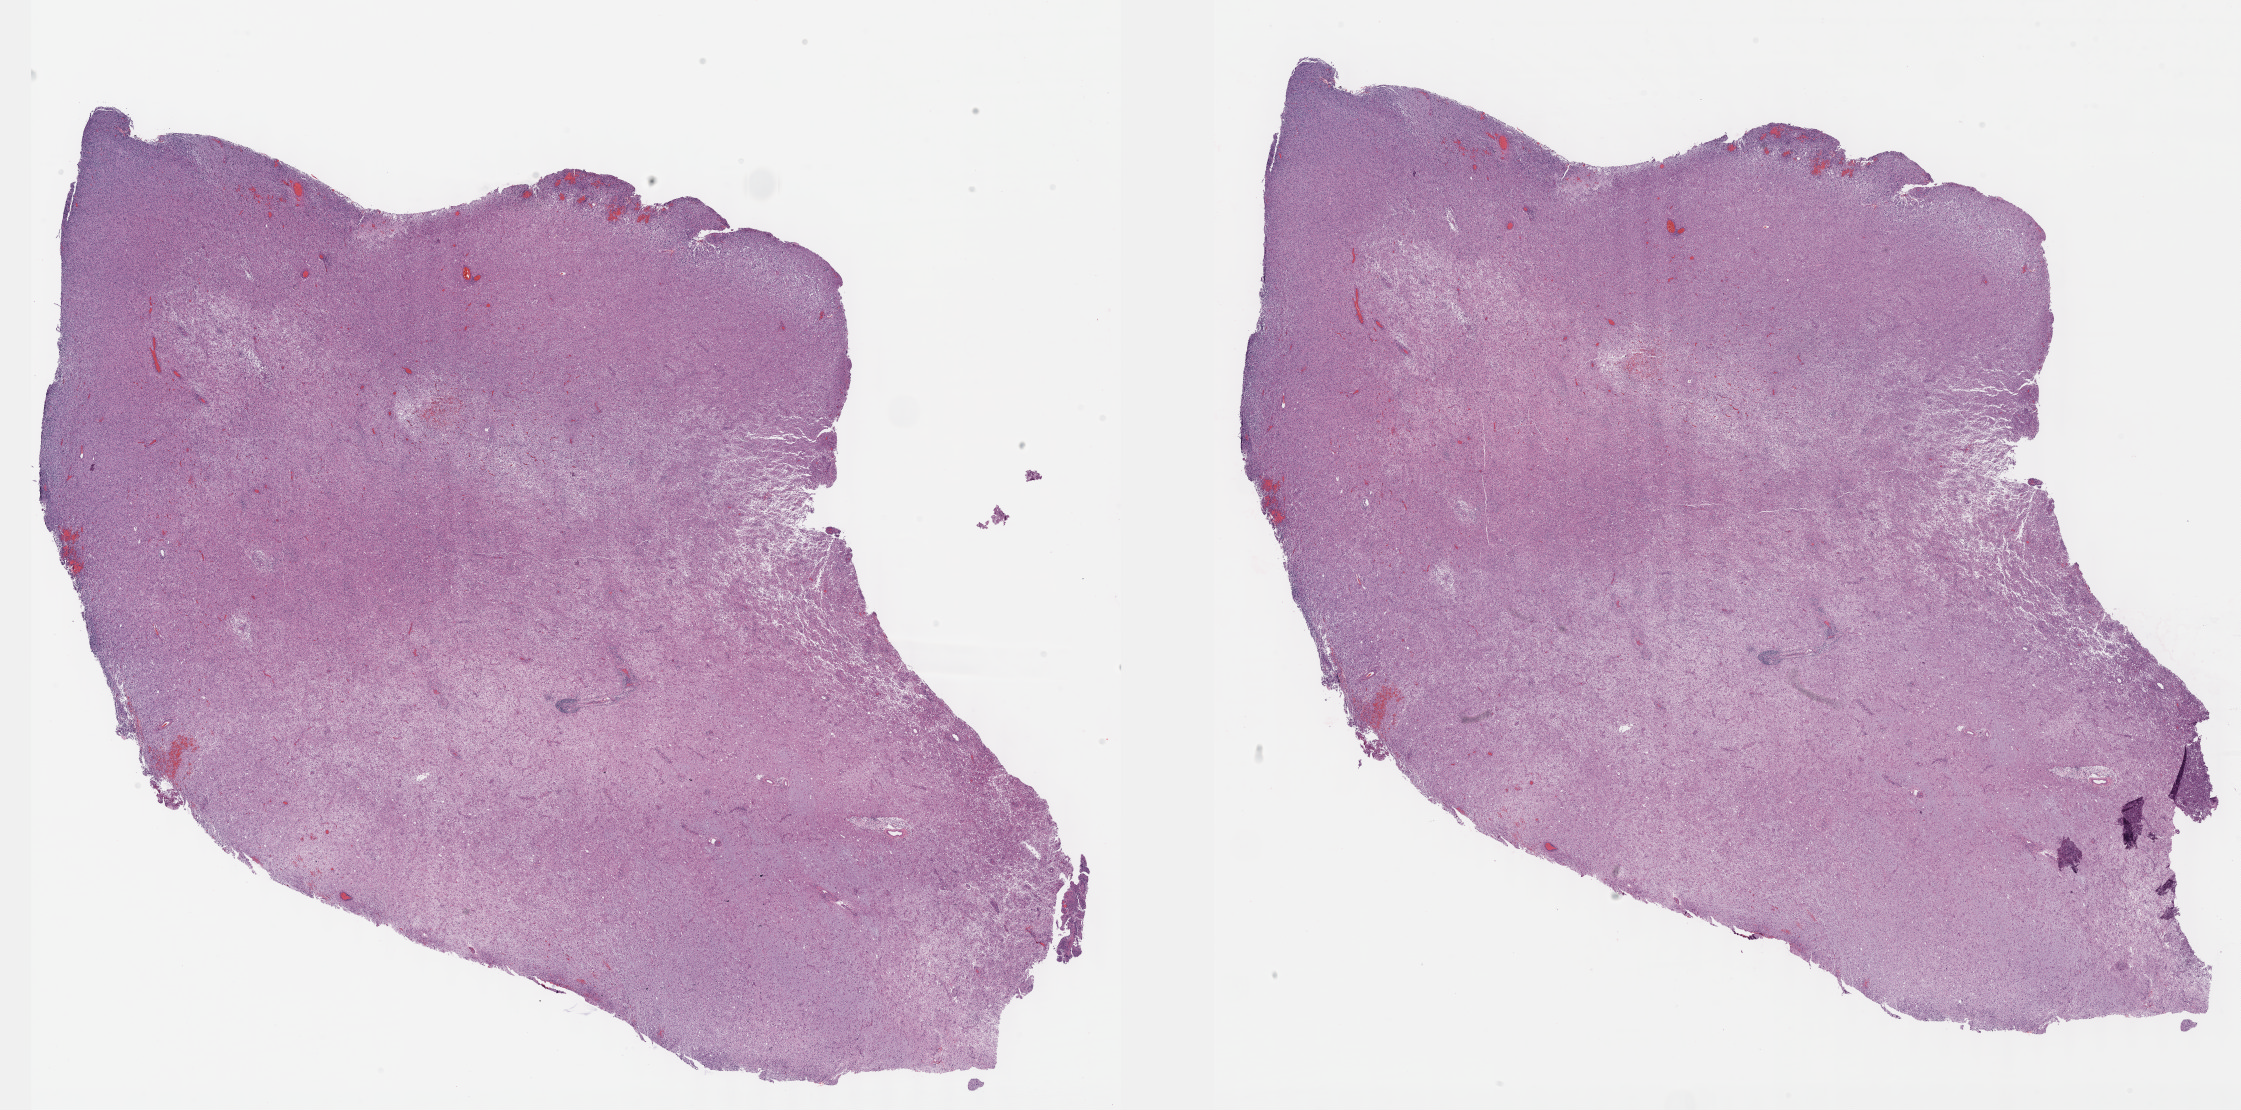
Digitized H&E tissue section (whole slide) — whole scanned area (about 36.2 x 17.9 mm, slide scanned at 40x) shown as a low-resolution overview. Formalin-fixed paraffin-embedded (FFPE) diagnostic section. Brain, primary tumour sample. Female patient; age at initial diagnosis 52 years. Histologic grade: G3 (poorly differentiated).
* laterality: right
* diagnosis: Astrocytoma, anaplastic (cerebrum)